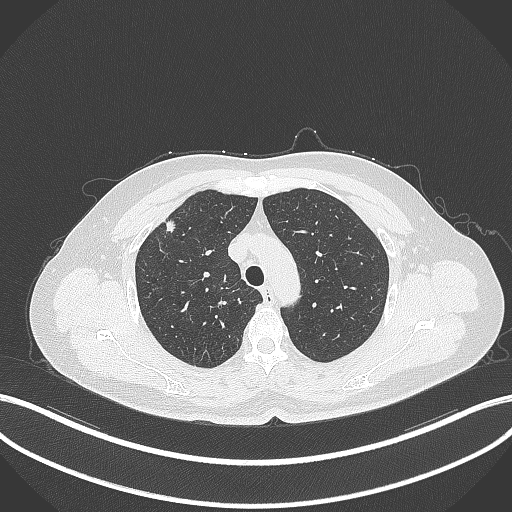
Chest CT, one axial slice. Position 280 of 353 along the scan axis. Reconstruction kernel B70f. Lung window (W 1500 / L -600 HU). 512 × 512 image matrix. Female patient, age 56 years. Case-level facts recorded for this patient, not image findings: clinical TNM (as recorded): T1c N0 M0.
Outlined on this slice (bounding box drawn by a radiologist):
- lung tumour (recorded histology: adenocarcinoma): bounding box (x1, y1, x2, y2) in pixels: (162, 217, 182, 240)